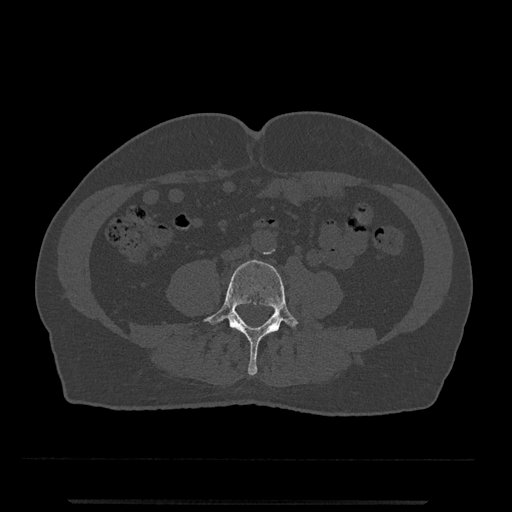
CT including the spine, one axial slice; slice 140 of 797 in the series (ordered by position); bone window (W 1800 / L 400 HU); 0.5 mm slice thickness; 512 × 512 image matrix, field of view 419 × 419 mm. Male patient, age 63 years. From the clinical record (not read from this slice): primary cancer: prostate.
Annotated regions visible in this slice (semi-automatic segmentation, software-assisted and operator-edited):
- L4 vertebra: bounding box [x1, y1, x2, y2] px = [202, 260, 299, 375]